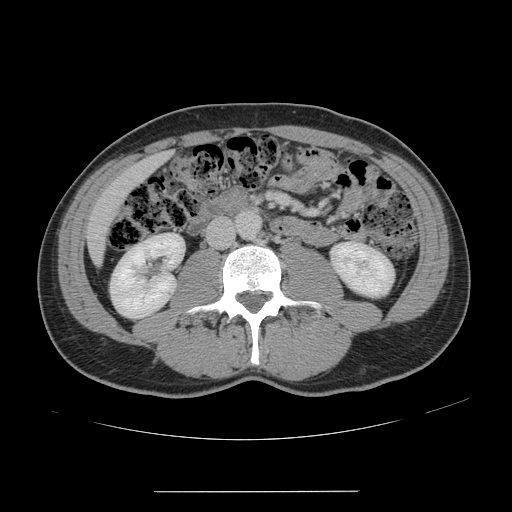
Contrast-enhanced abdominal CT, one axial slice; position 36 of 178 along the scan axis; 120 kVp; intravenous contrast given; soft-tissue window (W 400 / L 40 HU); 2.5 mm slice thickness; 512 × 512 image matrix. Male patient, age 53 years. Case-level facts recorded for this patient, not image findings: diagnosis: colorectal cancer liver metastases, imaged before liver resection; multiple liver metastases: yes; largest metastasis: 2.4 cm.
Annotated regions visible in this slice (manually delineated by an expert):
- liver: bounding box [x1, y1, x2, y2] px = [89, 154, 167, 262]